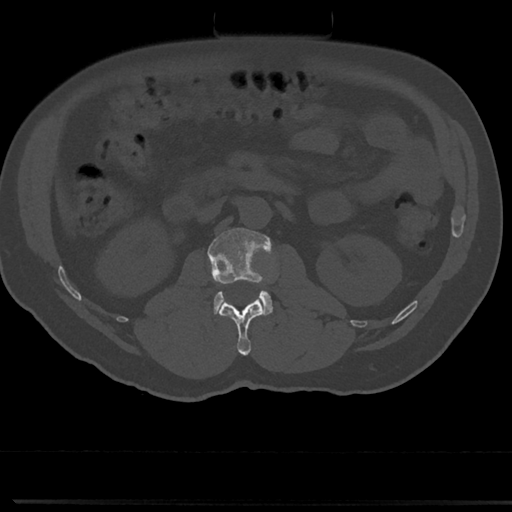
CT including the spine, one axial slice. Slice 45 of 817 in the series (ordered by position). Reconstruction kernel Br40s/3. Bone window (W 1800 / L 400 HU). 512 × 512 image matrix, field of view 355 × 355 mm. Patient: male, 61 years. From the clinical record (not read from this slice): primary cancer: prostate.
Annotated regions visible in this slice (semi-automatically segmented with operator editing):
- L1 vertebra: box from (x=219, y=299) to (x=264, y=355) px
- L2 vertebra: (x=208, y=227)–(x=272, y=316)